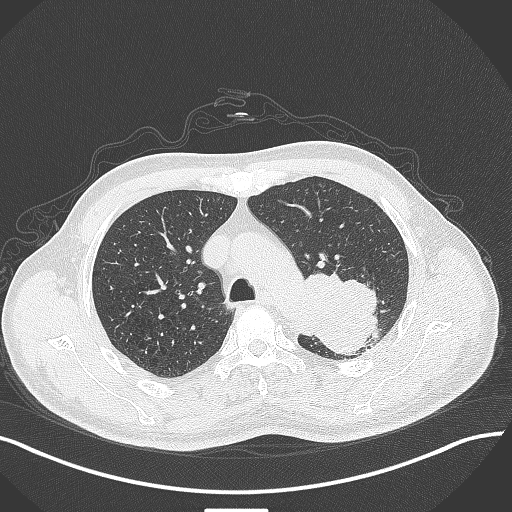
Chest CT, one axial slice. Position 311 of 429 along the scan axis. Reconstruction kernel B70f. 120 kVp. Lung window (W 1500 / L -600 HU). 1 mm slice thickness. 512 × 512 image matrix. Male patient, age 55 years. From the clinical record (not read from this slice): clinical TNM (as recorded): T3 N0 M1c; histopathological grade: G3.
Outlined on this slice (rectangle marked by the reading radiologist):
- lung tumour (recorded histology: adenocarcinoma): bounding box (x1, y1, x2, y2) in pixels: (294, 263, 383, 358)